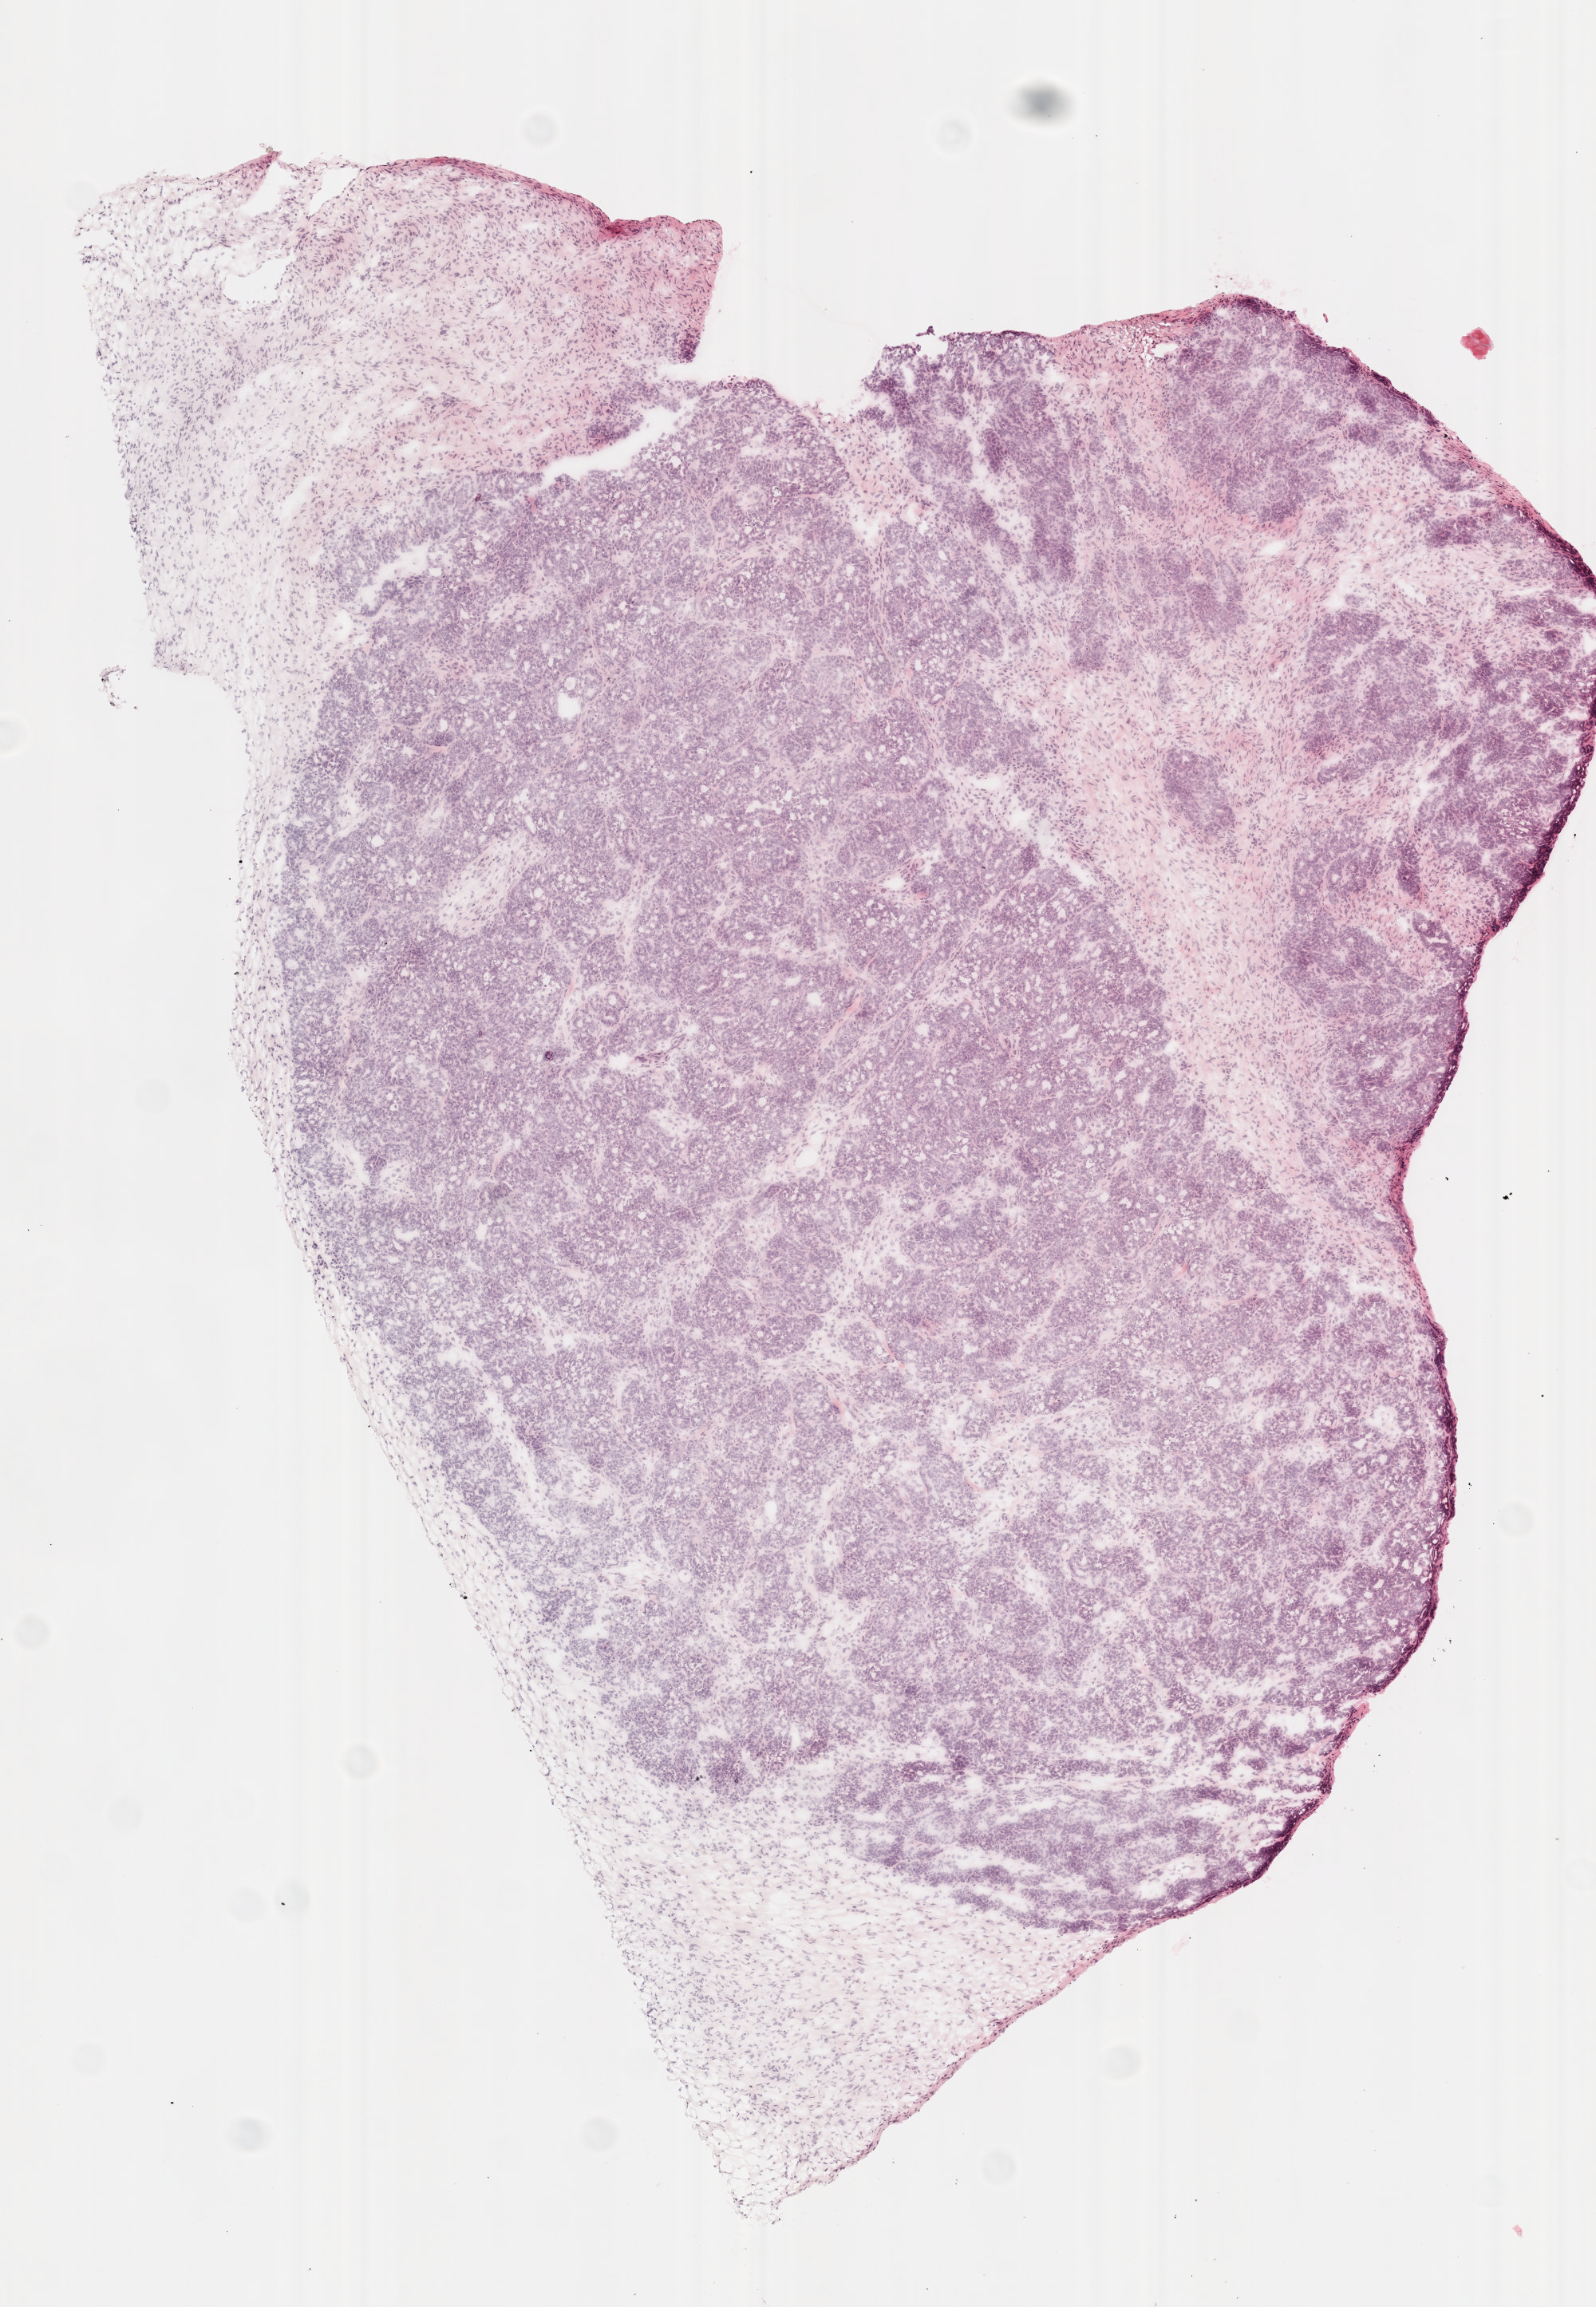
Whole-slide histology image, H&E — shown as a low-resolution overview of the whole scanned area (about 4.0 x 5.8 mm, from a 20x scan). Frozen section. Sample: primary tumour, ovary. Female patient; age at initial diagnosis 72 years.
Pathologic diagnosis: Serous cystadenocarcinoma, NOS.